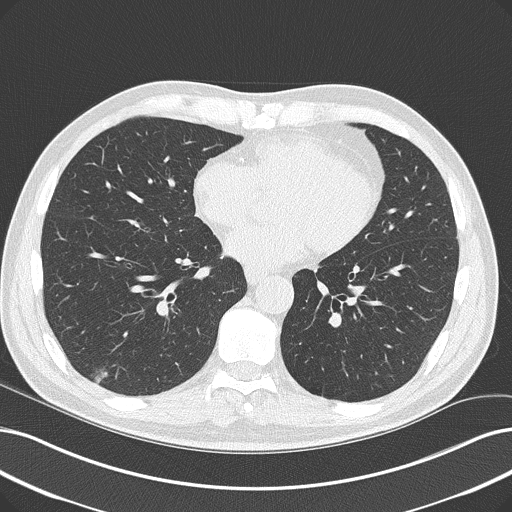
Low-dose screening chest CT, one axial slice; slice 95 of 228 in the series (ordered by position); reconstruction kernel B50f; lung window (W 1500 / L -600 HU); 2 mm slice thickness; 512 × 512 image matrix, field of view 366 × 366 mm.
Structures marked on this image (manually delineated by an expert):
- lesion 1 (tumor, lower lobe of right lung): bounding box [x1, y1, x2, y2] px = [95, 370, 108, 384]